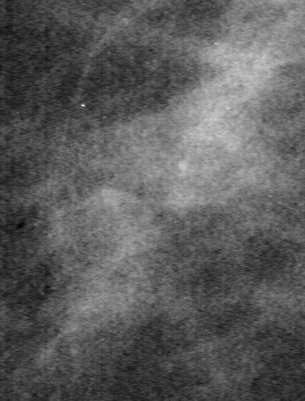
Cropped region of a digitized screen-film mammogram centred on a radiologist-marked abnormality; left breast; MLO view.
- Marked abnormality: calcifications, morphology pleomorphic, distribution clustered; BI-RADS assessment category 4; subtlety rating 1 on a 1 (subtle) to 5 (obvious) scale; pathology result (as recorded, not read from the image): malignant.